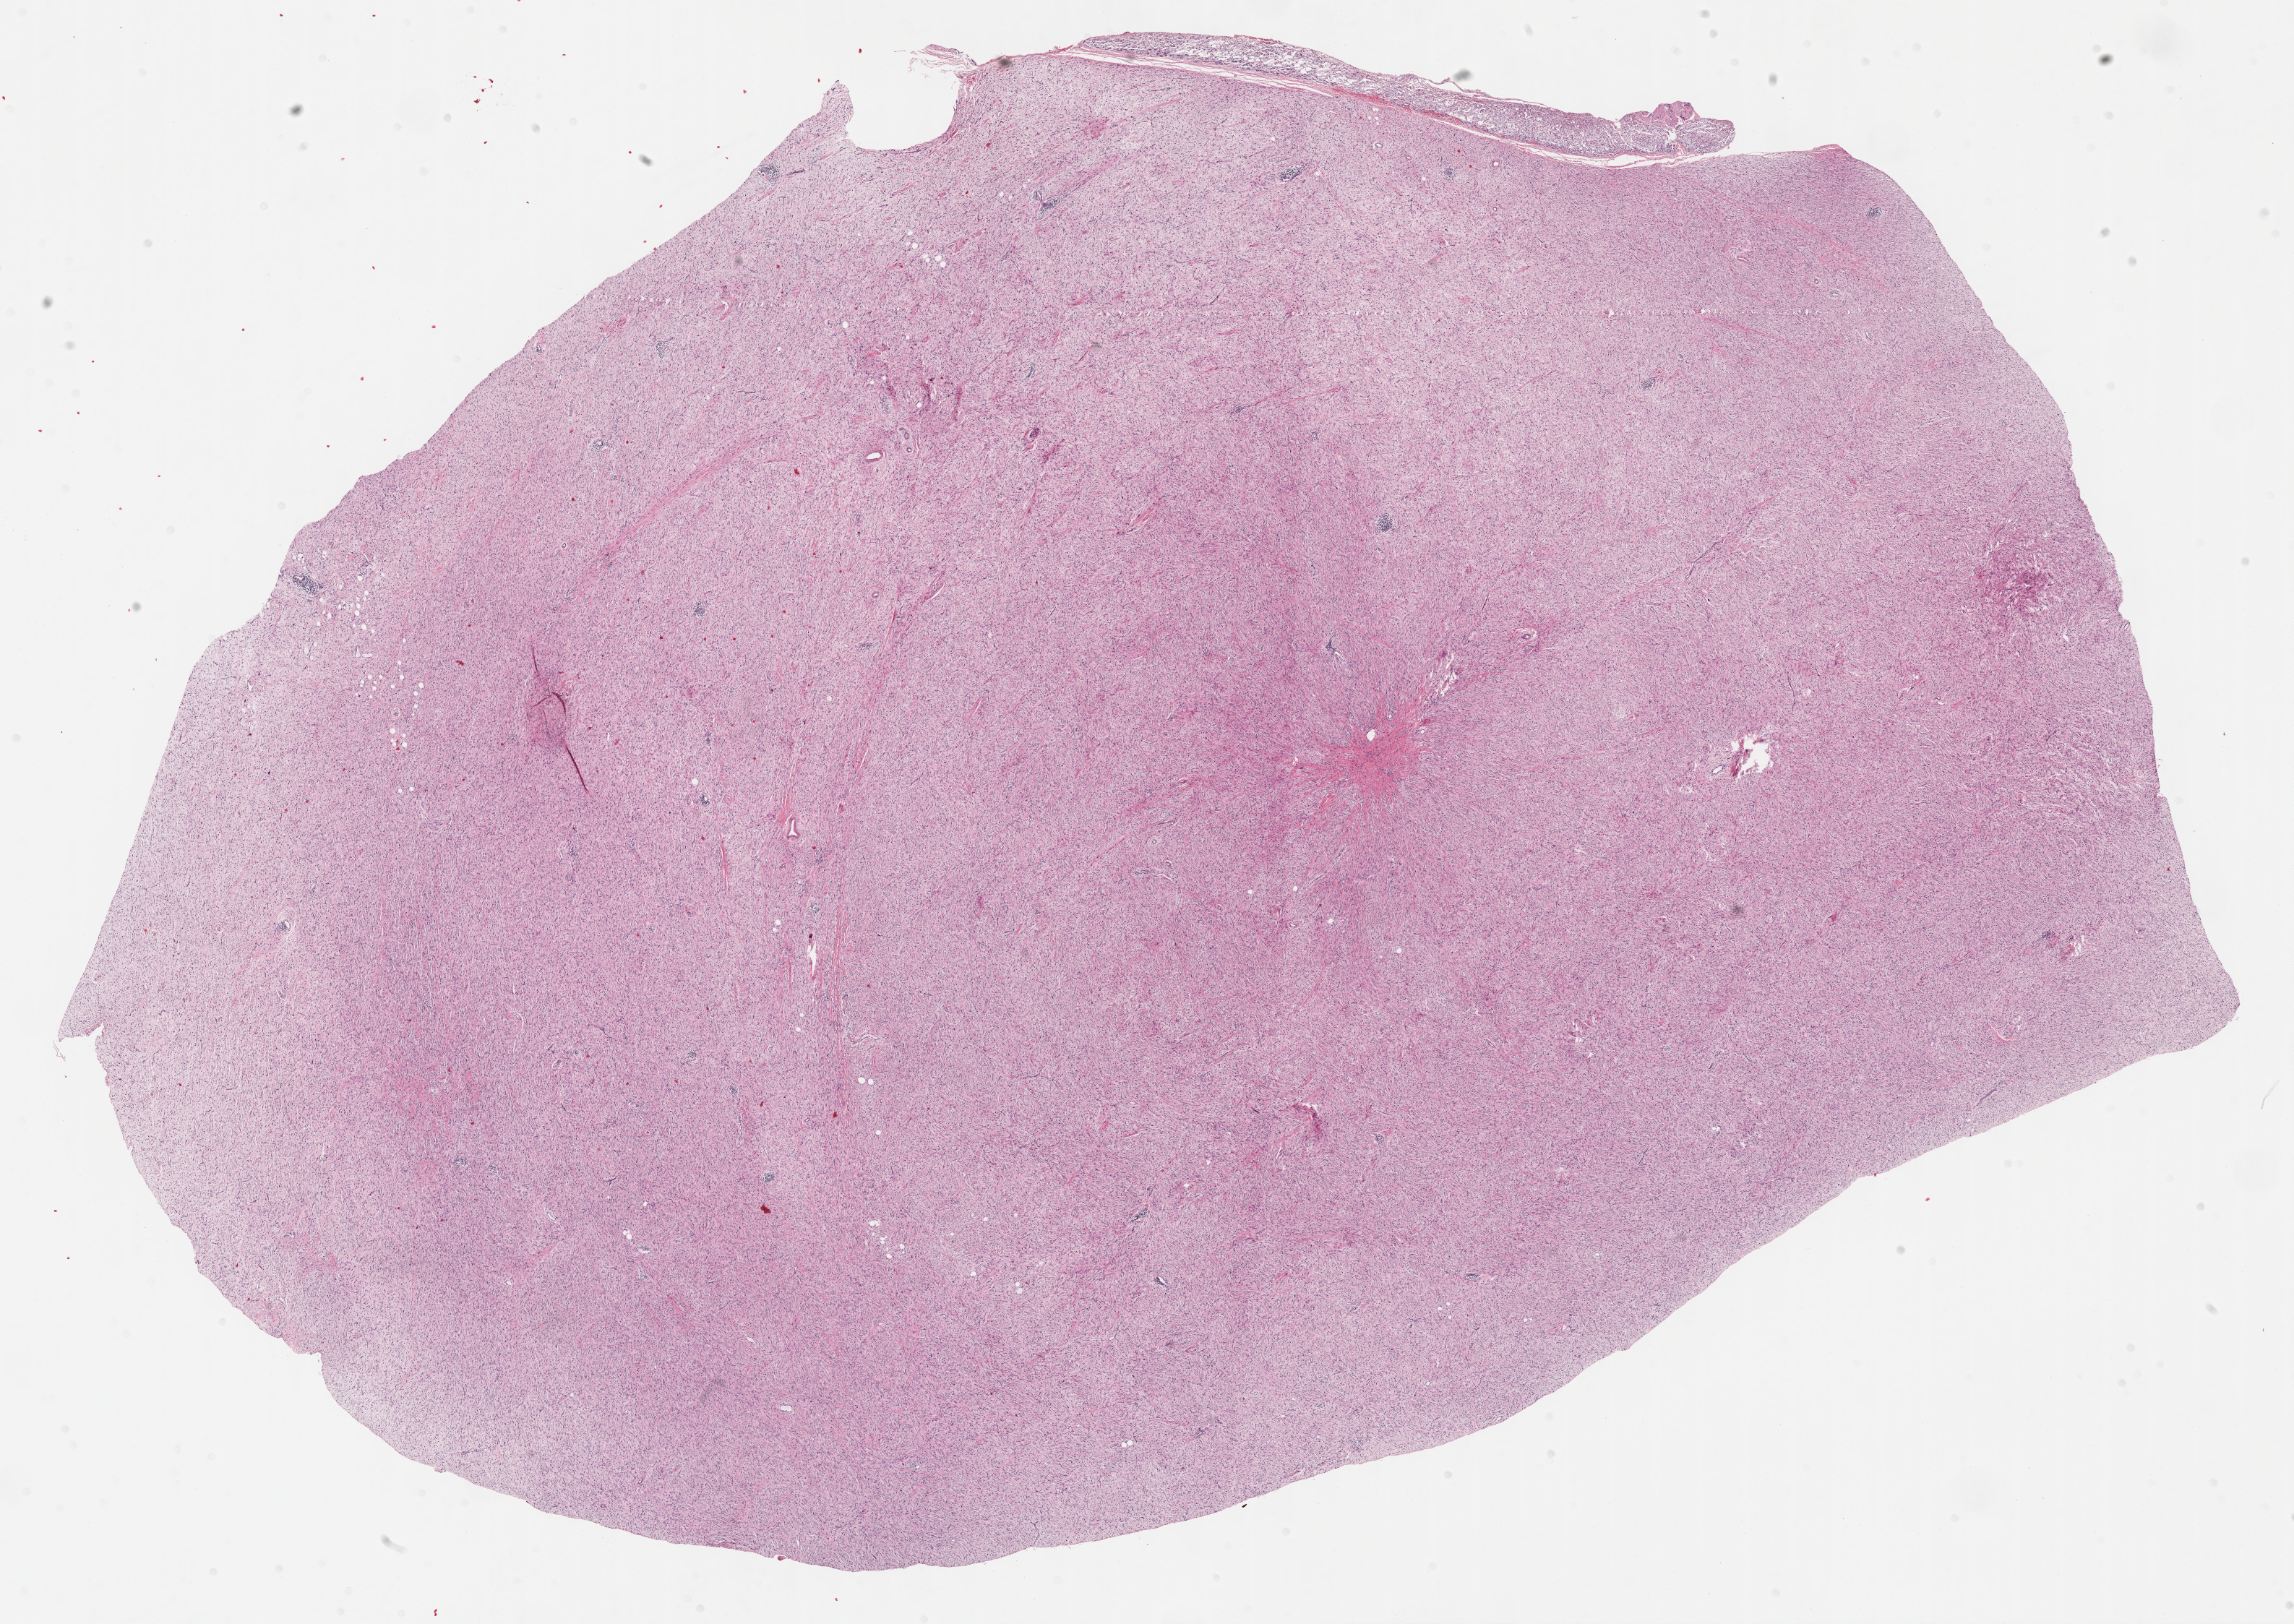
H&E whole-slide image, low-resolution overview of the scanned area, about 25.7 x 18.2 mm (from a 40x scan), FFPE section, sample: primary tumour, retroperitoneum and peritoneum. Male patient; age at initial diagnosis 36 years.
• histologic diagnosis: Dedifferentiated liposarcoma (retroperitoneum)